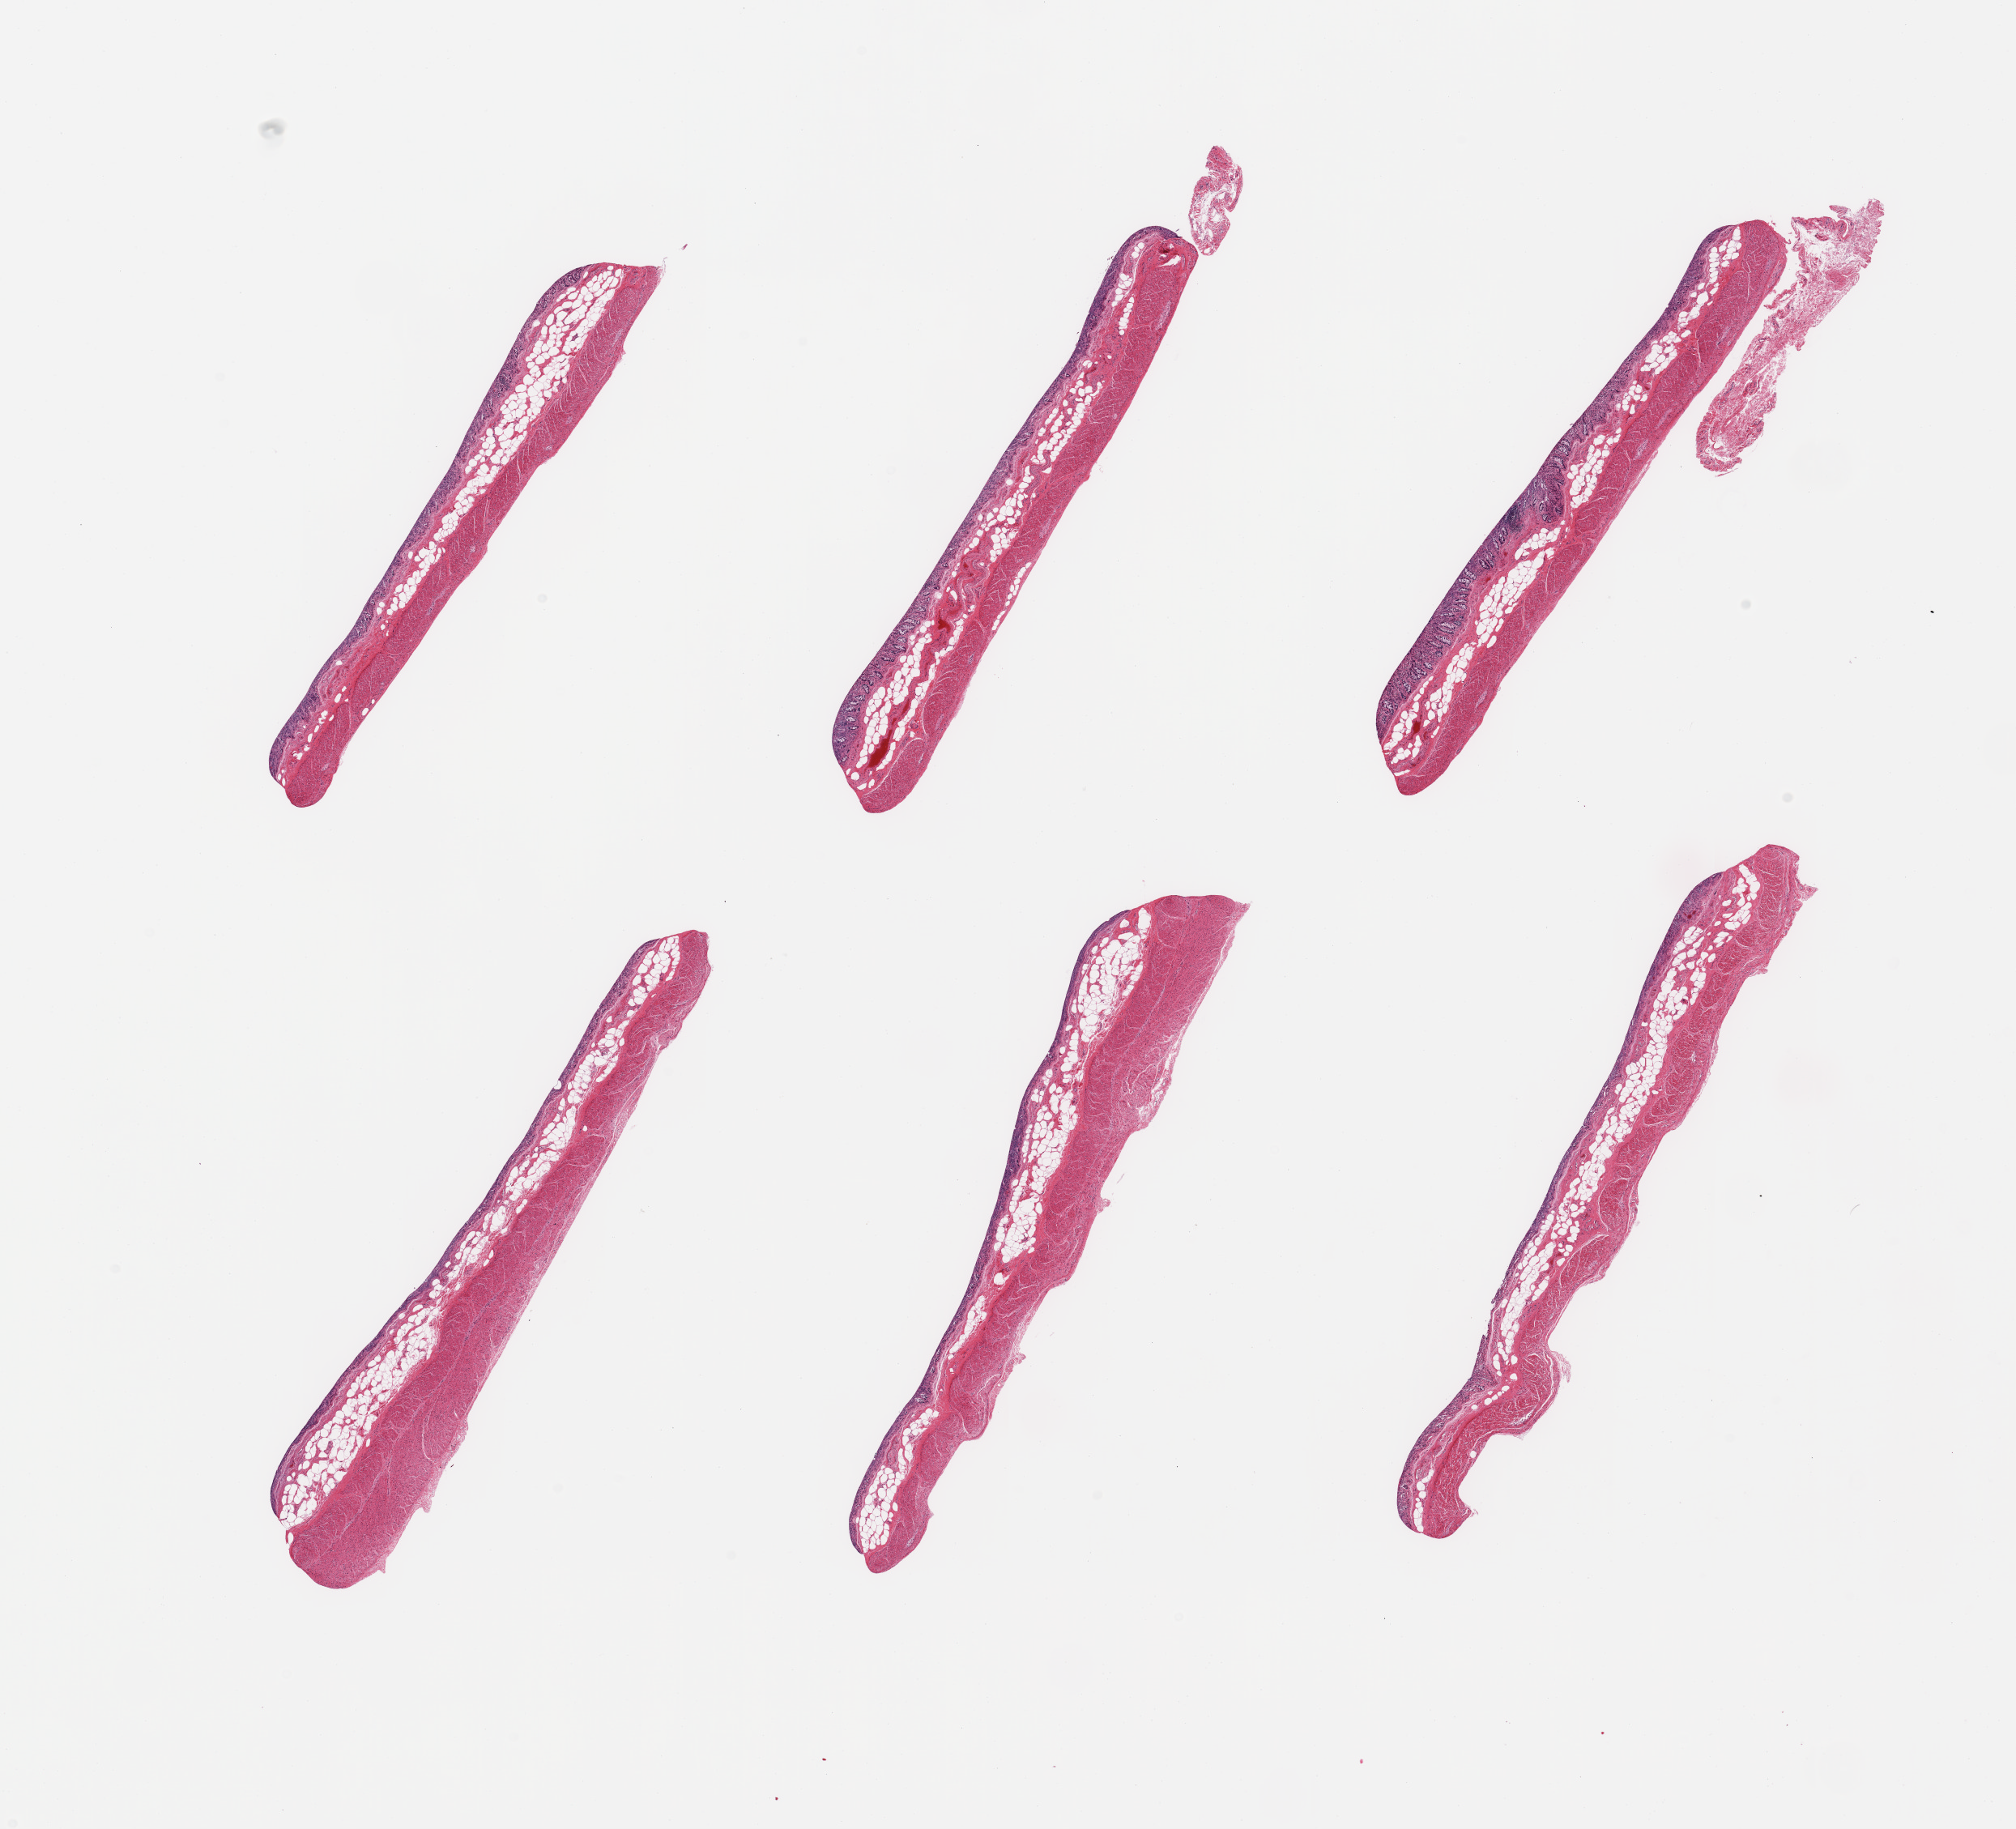
Whole-slide image, H&E stain, low-resolution overview of the scanned area, about 19.7 x 17.9 mm (slide scanned at 20x), PAXgene-fixed, paraffin-embedded tissue, section of transverse colon (target tissue), tissue donor sample. Donor sex: male.
Reviewer comment on this tissue sample: 6 pieces; largely sloughed mucosa and fatty submucosa on all.